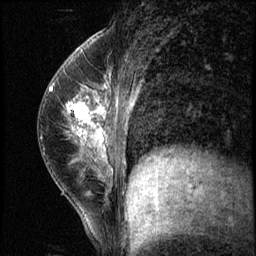
Breast MRI (dynamic contrast-enhanced), one sagittal slice; slice 28 of 56 in the series (ordered by position); 3 images stored at this slice position (order not interpretable as contrast timing); 1.5 T; TE 4.2 ms, TR 8.7 ms; 2.5 mm slice thickness; 256 × 256 image matrix, field of view 180 × 180 mm. Female patient, age 35 years. From the clinical record (not read from this slice): setting: breast cancer imaged before/during neoadjuvant chemotherapy; receptor status: HER2-positive.
Annotated regions visible in this slice (semi-automatic segmentation, software-assisted and operator-edited):
- analysis volume of interest (the breast-tissue region the enhancement analysis was run in; not a lesion): bounding box [x1, y1, x2, y2] px = [58, 84, 138, 186]
- tumour enhancement mask (voxels above the 140 % enhancement threshold inside the analysis volume of interest): [65, 86, 108, 152]